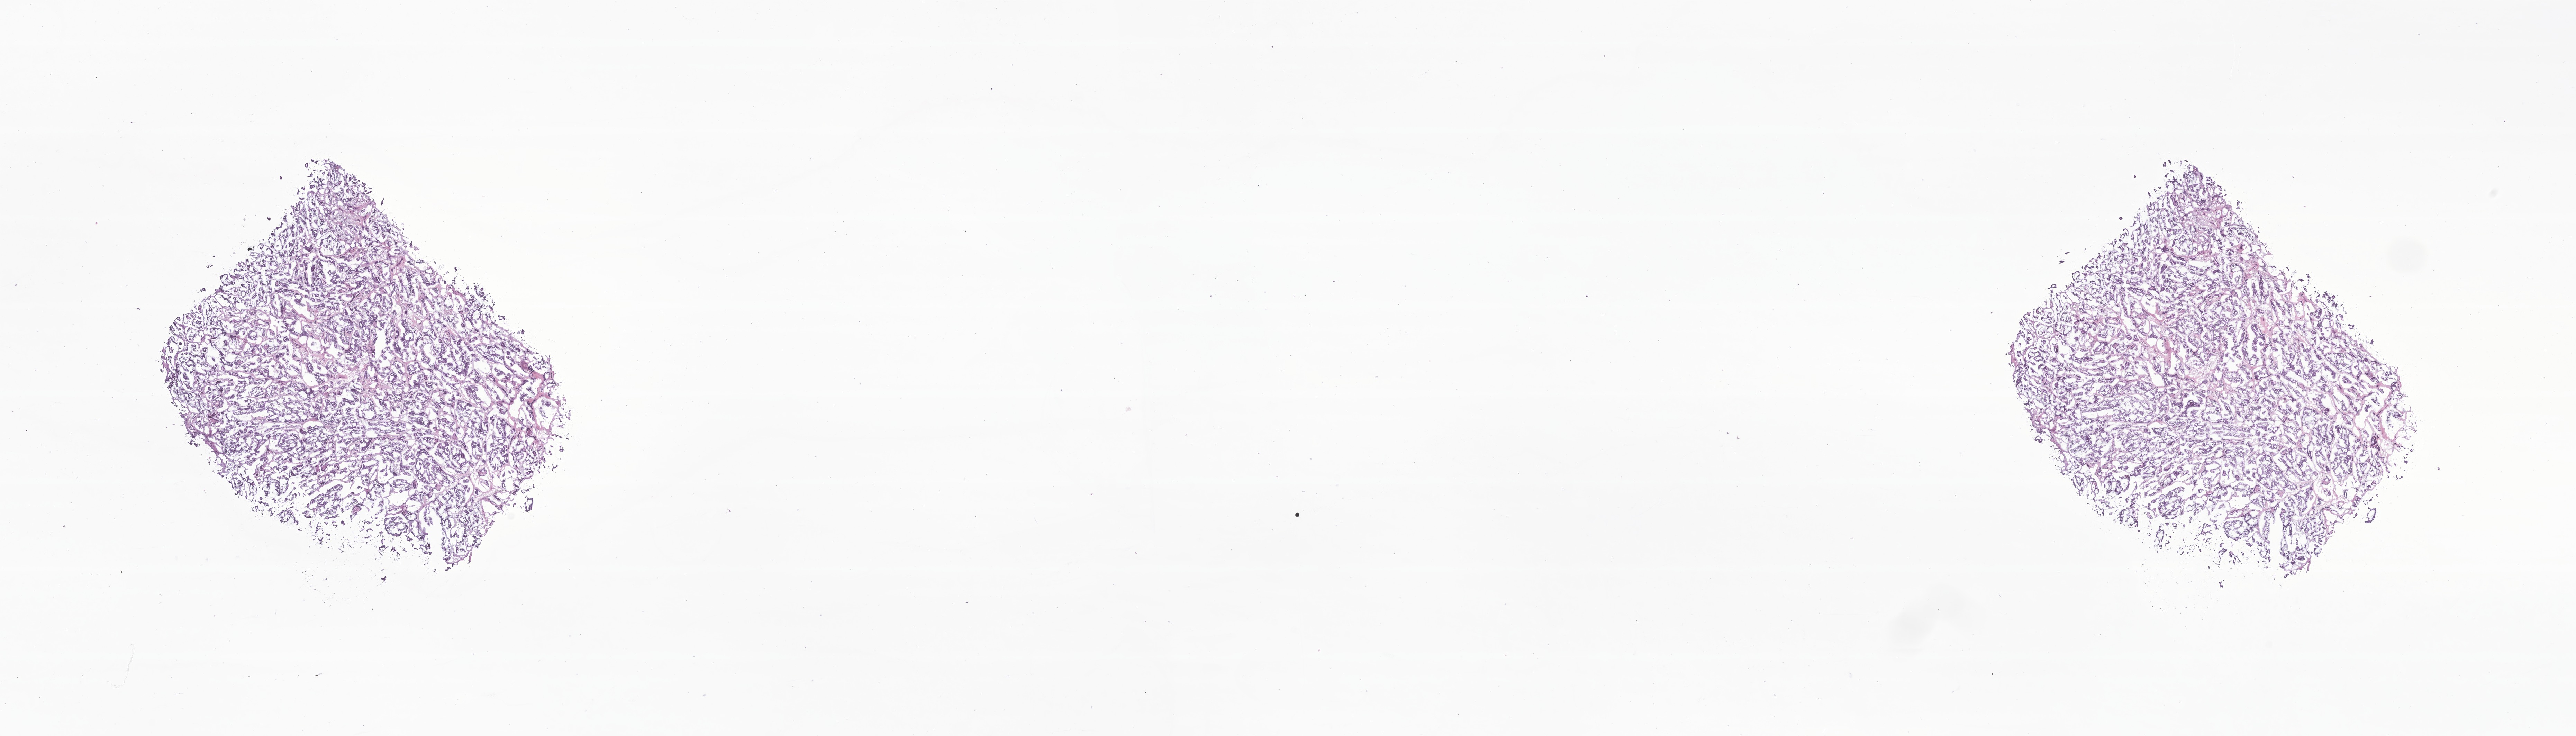
Digitized hematoxylin and eosin (H&E)-stained section of tumor tissue from the lacrimal gland — shown as a low-resolution overview of the whole scanned area (about 31.4 x 9.0 mm). Frozen section. Male patient, age 142 months (11 years 10 months).
- diagnosis (ICD-O-3 morphology term): Adenoid cystic carcinoma